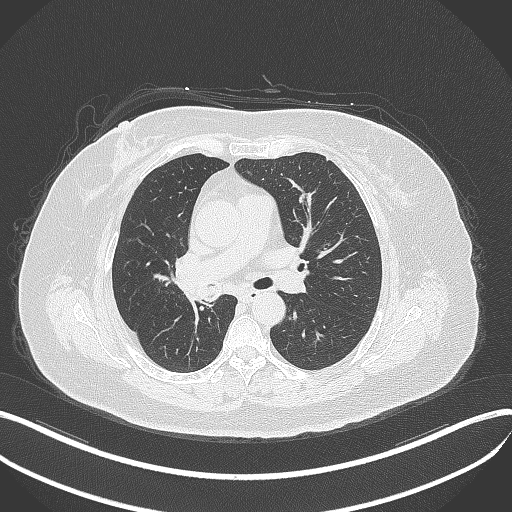
Chest CT, one axial slice; position 211 of 376 along the scan axis; reconstruction kernel B70f; lung window (W 1500 / L -600 HU); 1 mm slice thickness; 512 × 512 image matrix, field of view 400 × 400 mm. Patient: female, 60 years. From the clinical record (not read from this slice): clinical TNM (as recorded): T1c N0 M0.
Outlined on this slice (rectangle marked by the reading radiologist):
- lung tumour (recorded histology: squamous cell carcinoma): box from (x=178, y=277) to (x=223, y=306) px